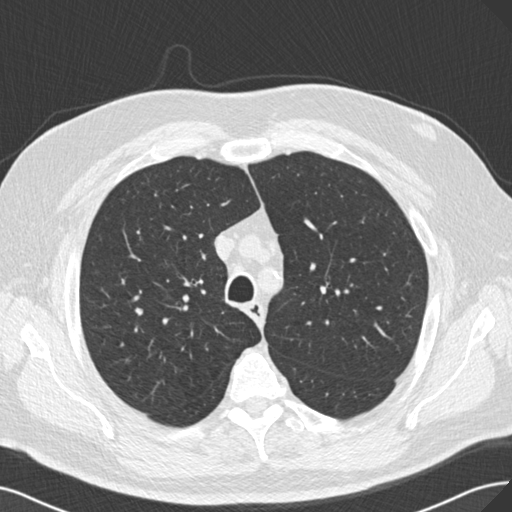
Low-dose screening chest CT, axial slice, baseline screening round, lung window (W 1500 / L -600 HU), slice 45 of 175 in the series. Male participant, aged 67 years at enrolment.
Expert-annotated lung lesion, bounding box (x1, y1, x2, y2) in pixels: (130, 303, 146, 321). No non-calcified nodule or mass ≥4 mm was recorded by the screening reader at this exam. Lung cancer was diagnosed 561 days after this screen: small cell carcinoma, NOS, right middle lobe, stage IA (AJCC 6th edition), 20 mm at pathology.